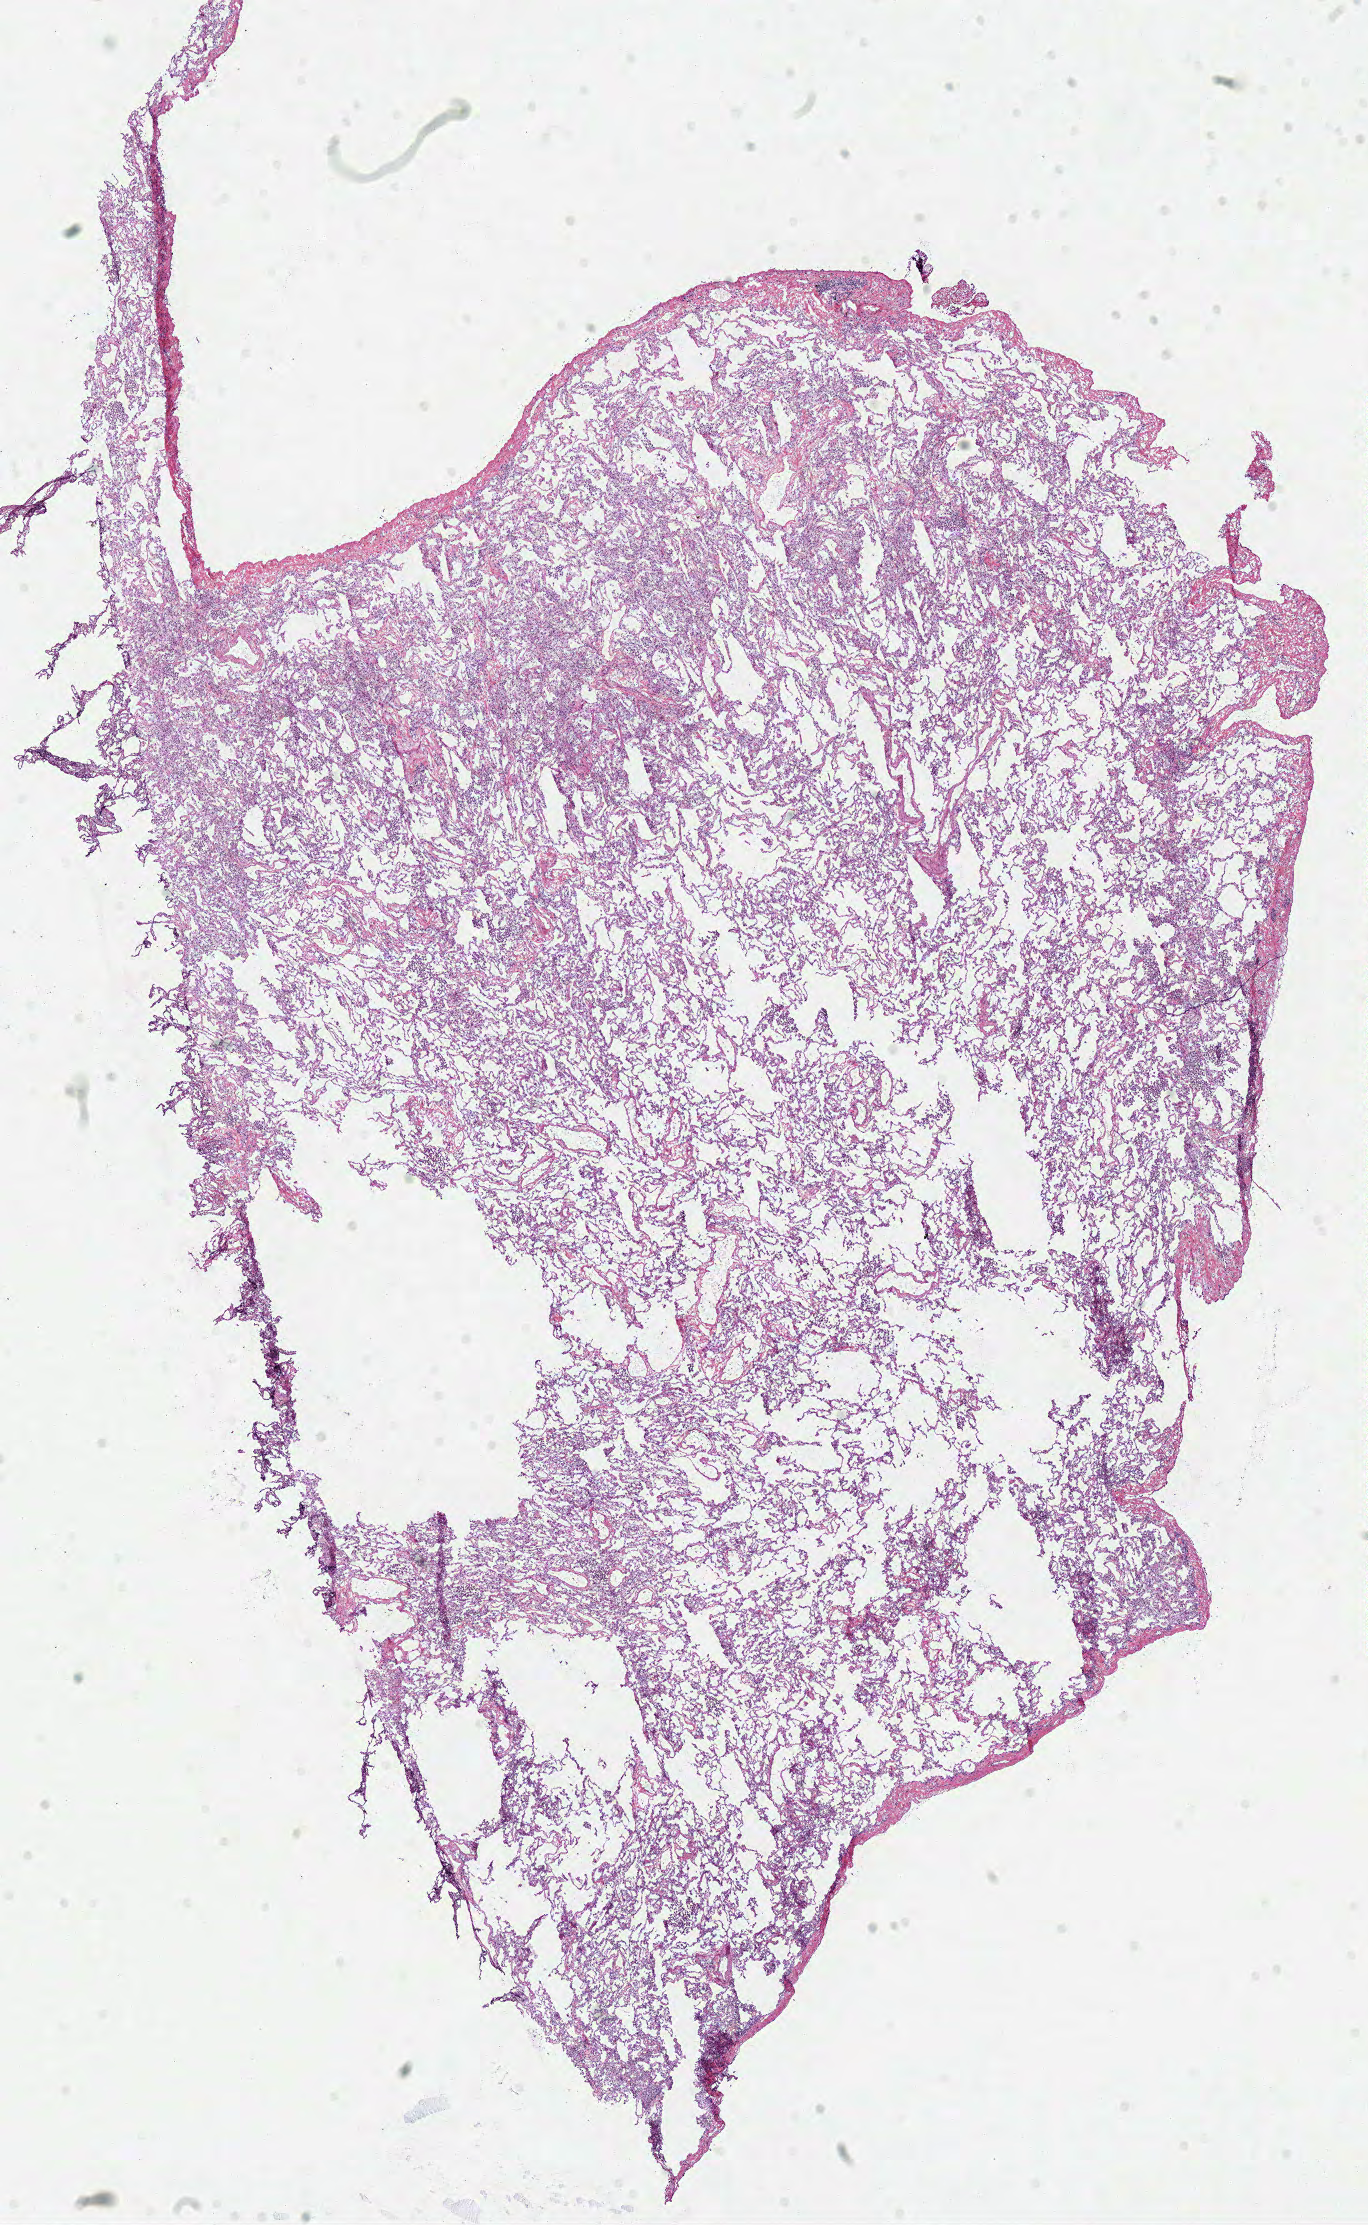
Whole-slide histology image, H&E-stained, shown as a low-resolution overview of the whole scanned area (about 10.8 x 17.5 mm, acquisition: 40x scan), frozen section from the top of the tissue portion, lung, solid tissue normal (non-tumour tissue) sample. Female patient; age at initial diagnosis 71 years.
This section: solid tissue normal sample (biorepository sample class). Patient diagnosis: Adenocarcinoma, NOS (lower lobe, lung).